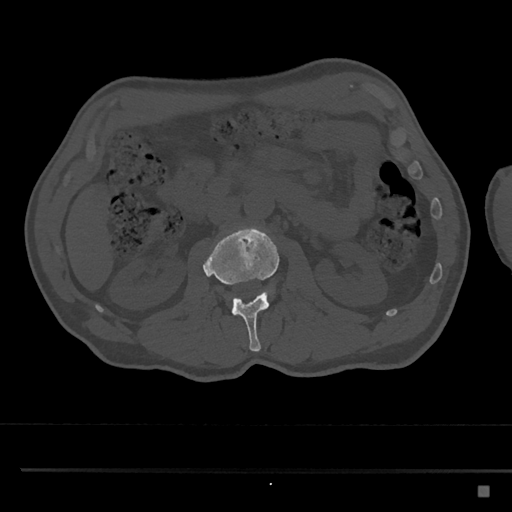
CT including the spine, one axial slice; slice 746 of 797 in the series (ordered by position); reconstruction kernel Br40s/3; 120 kVp; bone window (W 1800 / L 400 HU); 0.5 mm slice thickness; 512 × 512 image matrix, field of view 391 × 391 mm. Male patient, age 59 years. Case-level facts recorded for this patient, not image findings: primary cancer: prostate.
Annotated regions visible in this slice (semi-automatic segmentation, software-assisted and operator-edited):
- L2 vertebra: box from (x=203, y=226) to (x=280, y=352) px